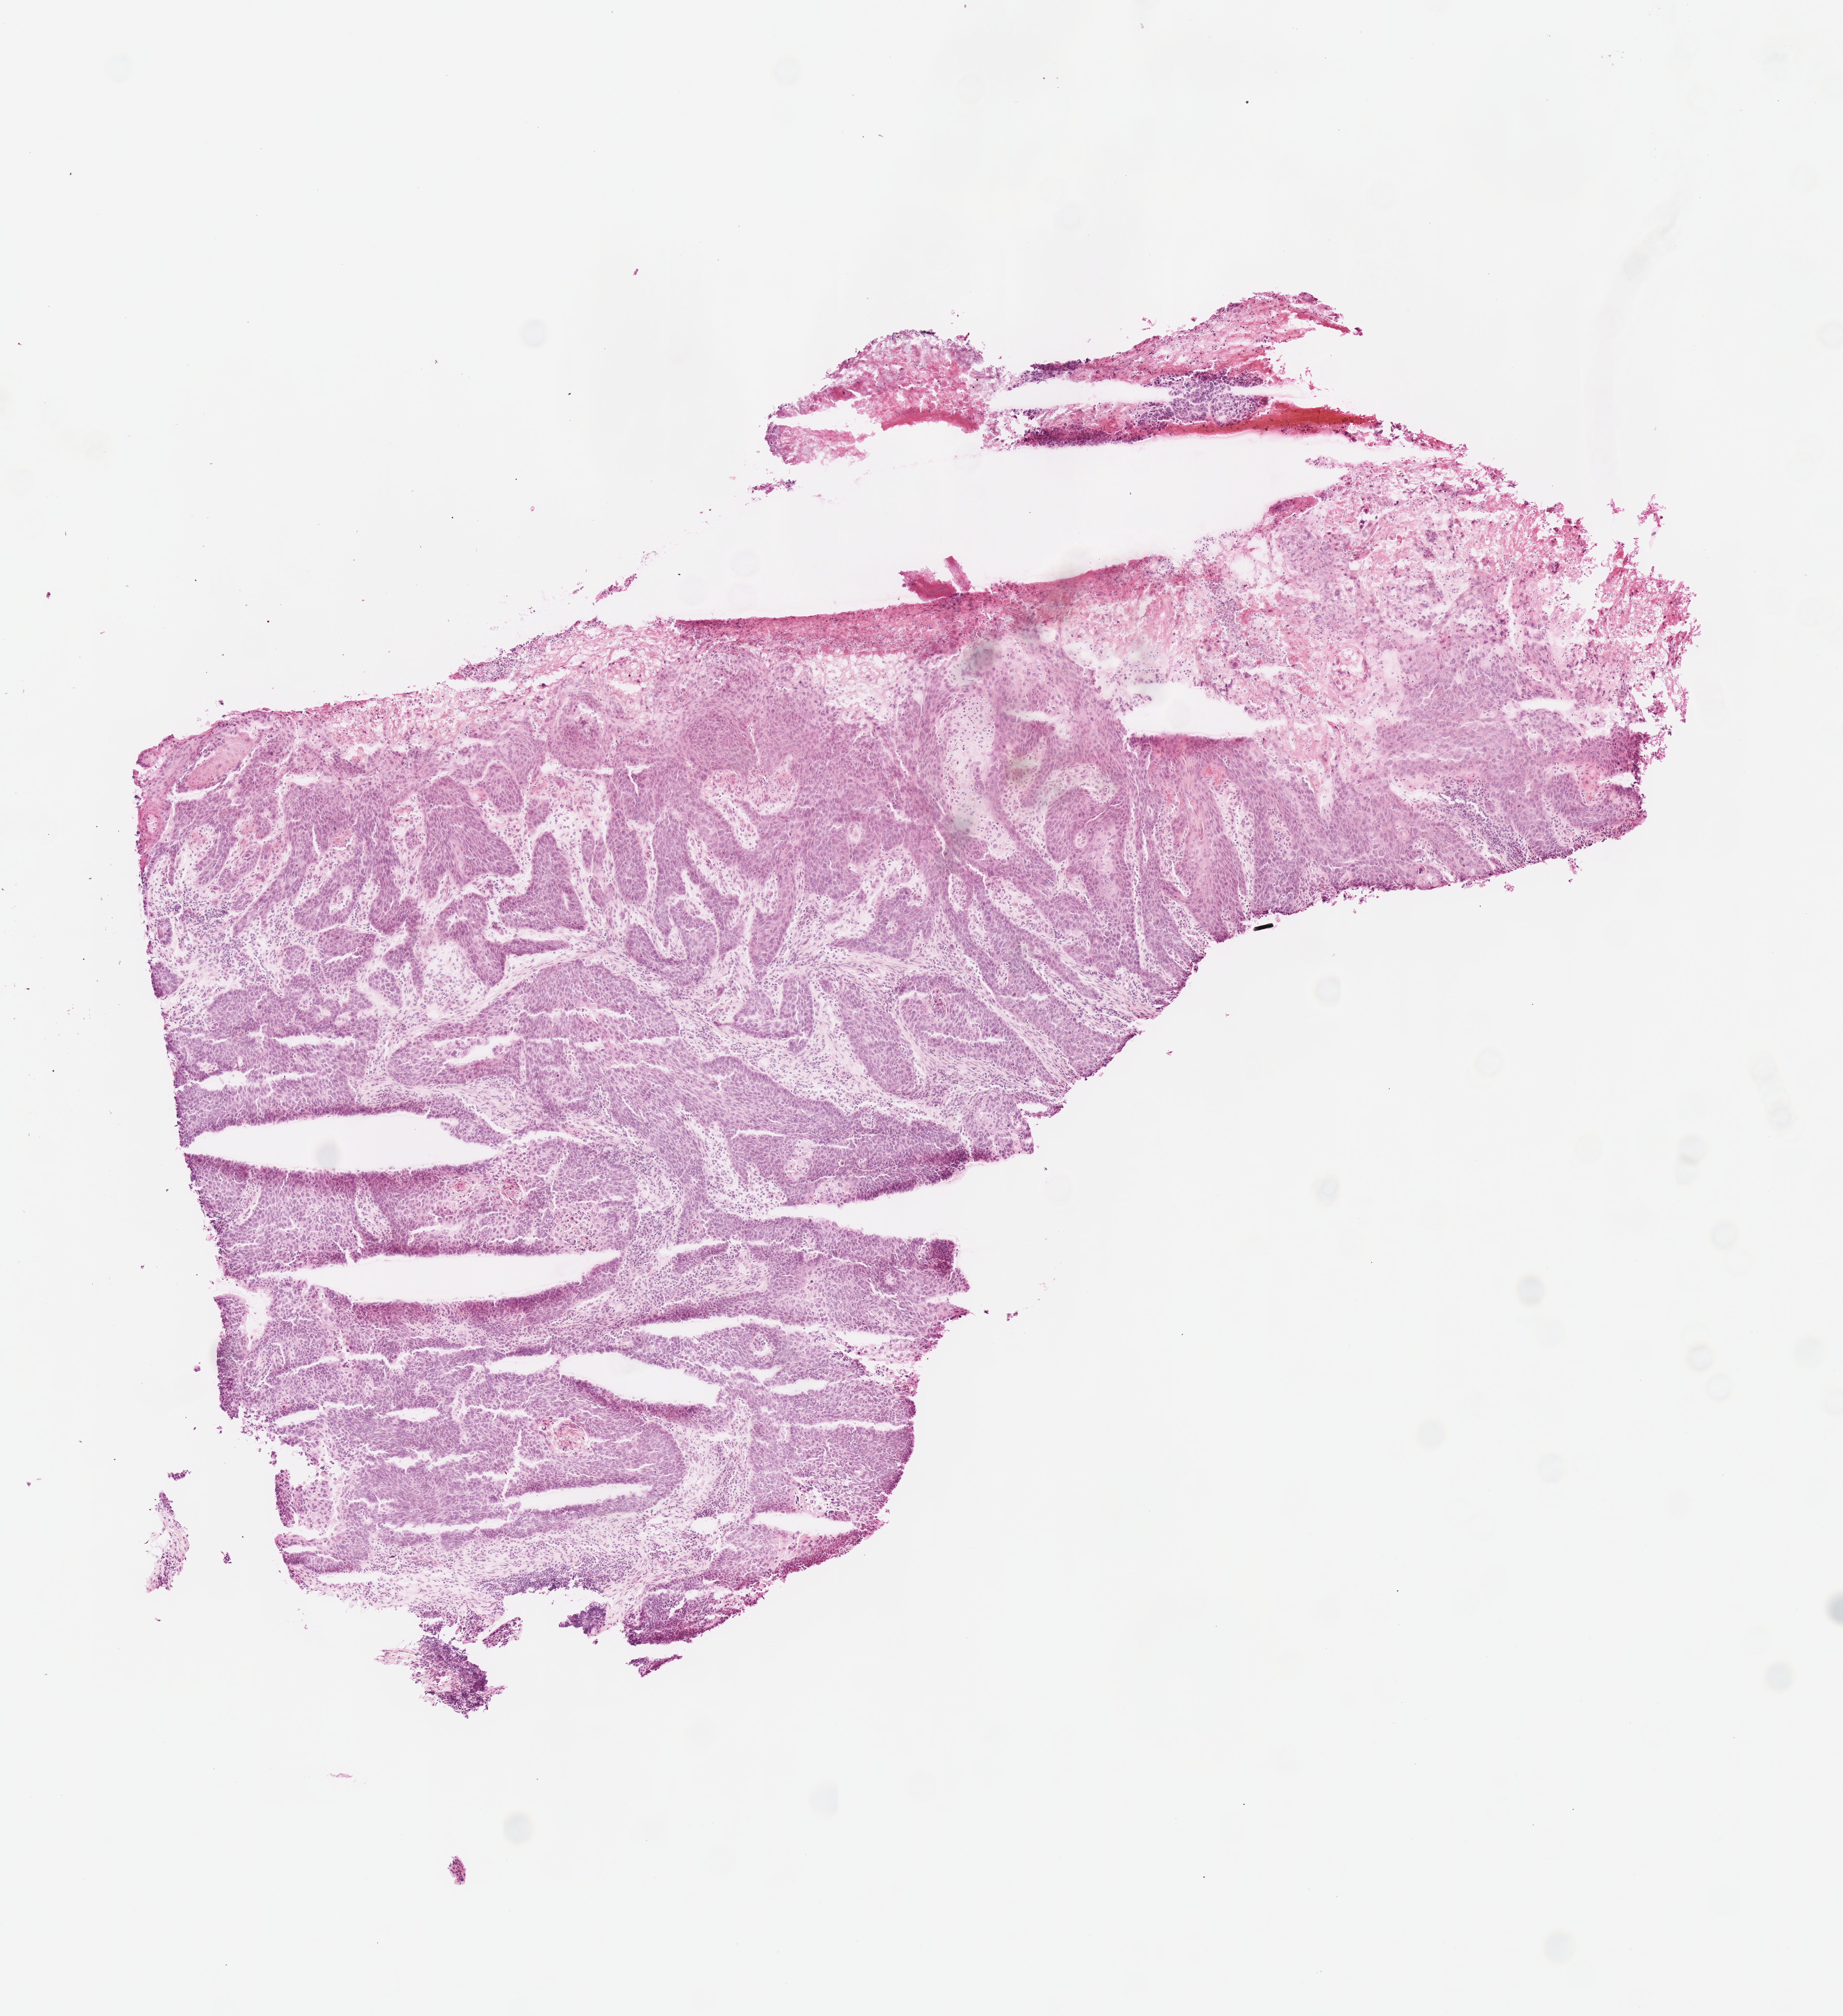
H&E whole-slide image, shown as a low-resolution overview of the whole scanned area (about 5.4 x 5.9 mm, acquisition: 40x scan), frozen section from the top of the tissue portion, head and neck, primary tumour sample. Patient: male, age at initial diagnosis 58 years. Histologic grade: G3 (poorly differentiated). Composition of this section per pathologist review: tumour cells 75%, tumour nuclei 75%, normal cells 0%, stromal cells 15%, necrosis 10%.
TNM: T4a N0. Histologic diagnosis: Squamous cell carcinoma, NOS (larynx, NOS). AJCC pathologic stage: IVA (7th edition). Lymph nodes positive (case pathology): 0 of 83 examined.